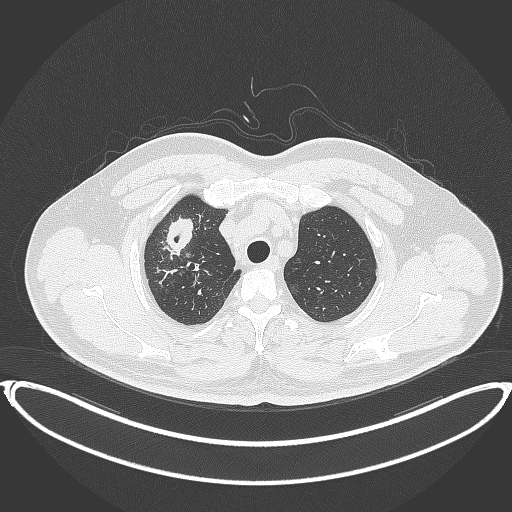
Chest CT, one axial slice; slice 324 of 399 in the series (ordered by position); reconstruction kernel B70f; 120 kVp; lung window (W 1500 / L -600 HU); 1 mm slice thickness; 512 × 512 image matrix, field of view 445 × 445 mm. Patient: male, 53 years. From the clinical record (not read from this slice): clinical TNM (as recorded): T2a N0 M0.
Outlined on this slice (bounding box drawn by a radiologist):
- lung tumour (recorded histology: adenocarcinoma): box from (x=161, y=214) to (x=198, y=256) px